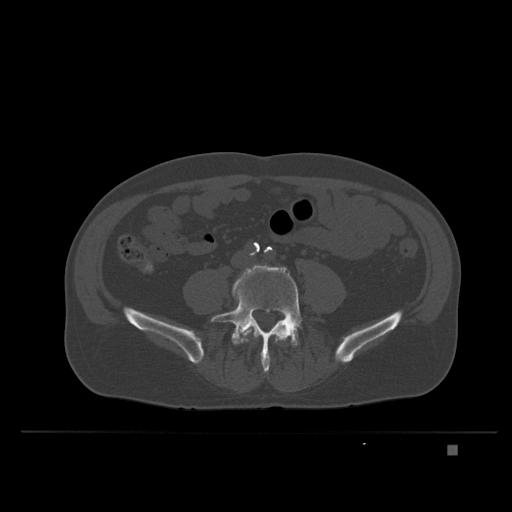
CT including the spine, one axial slice. Position 60 of 435 along the scan axis. Bone window (W 1800 / L 400 HU). 512 × 512 image matrix, field of view 434 × 434 mm. Patient: male, 73 years. Case-level facts recorded for this patient, not image findings: primary cancer: skin.
Annotated regions visible in this slice (semi-automatic segmentation, software-assisted and operator-edited):
- L4 vertebra: bounding box (x1, y1, x2, y2) in pixels: (243, 325, 269, 353)
- L5 vertebra: (210, 264, 303, 373)